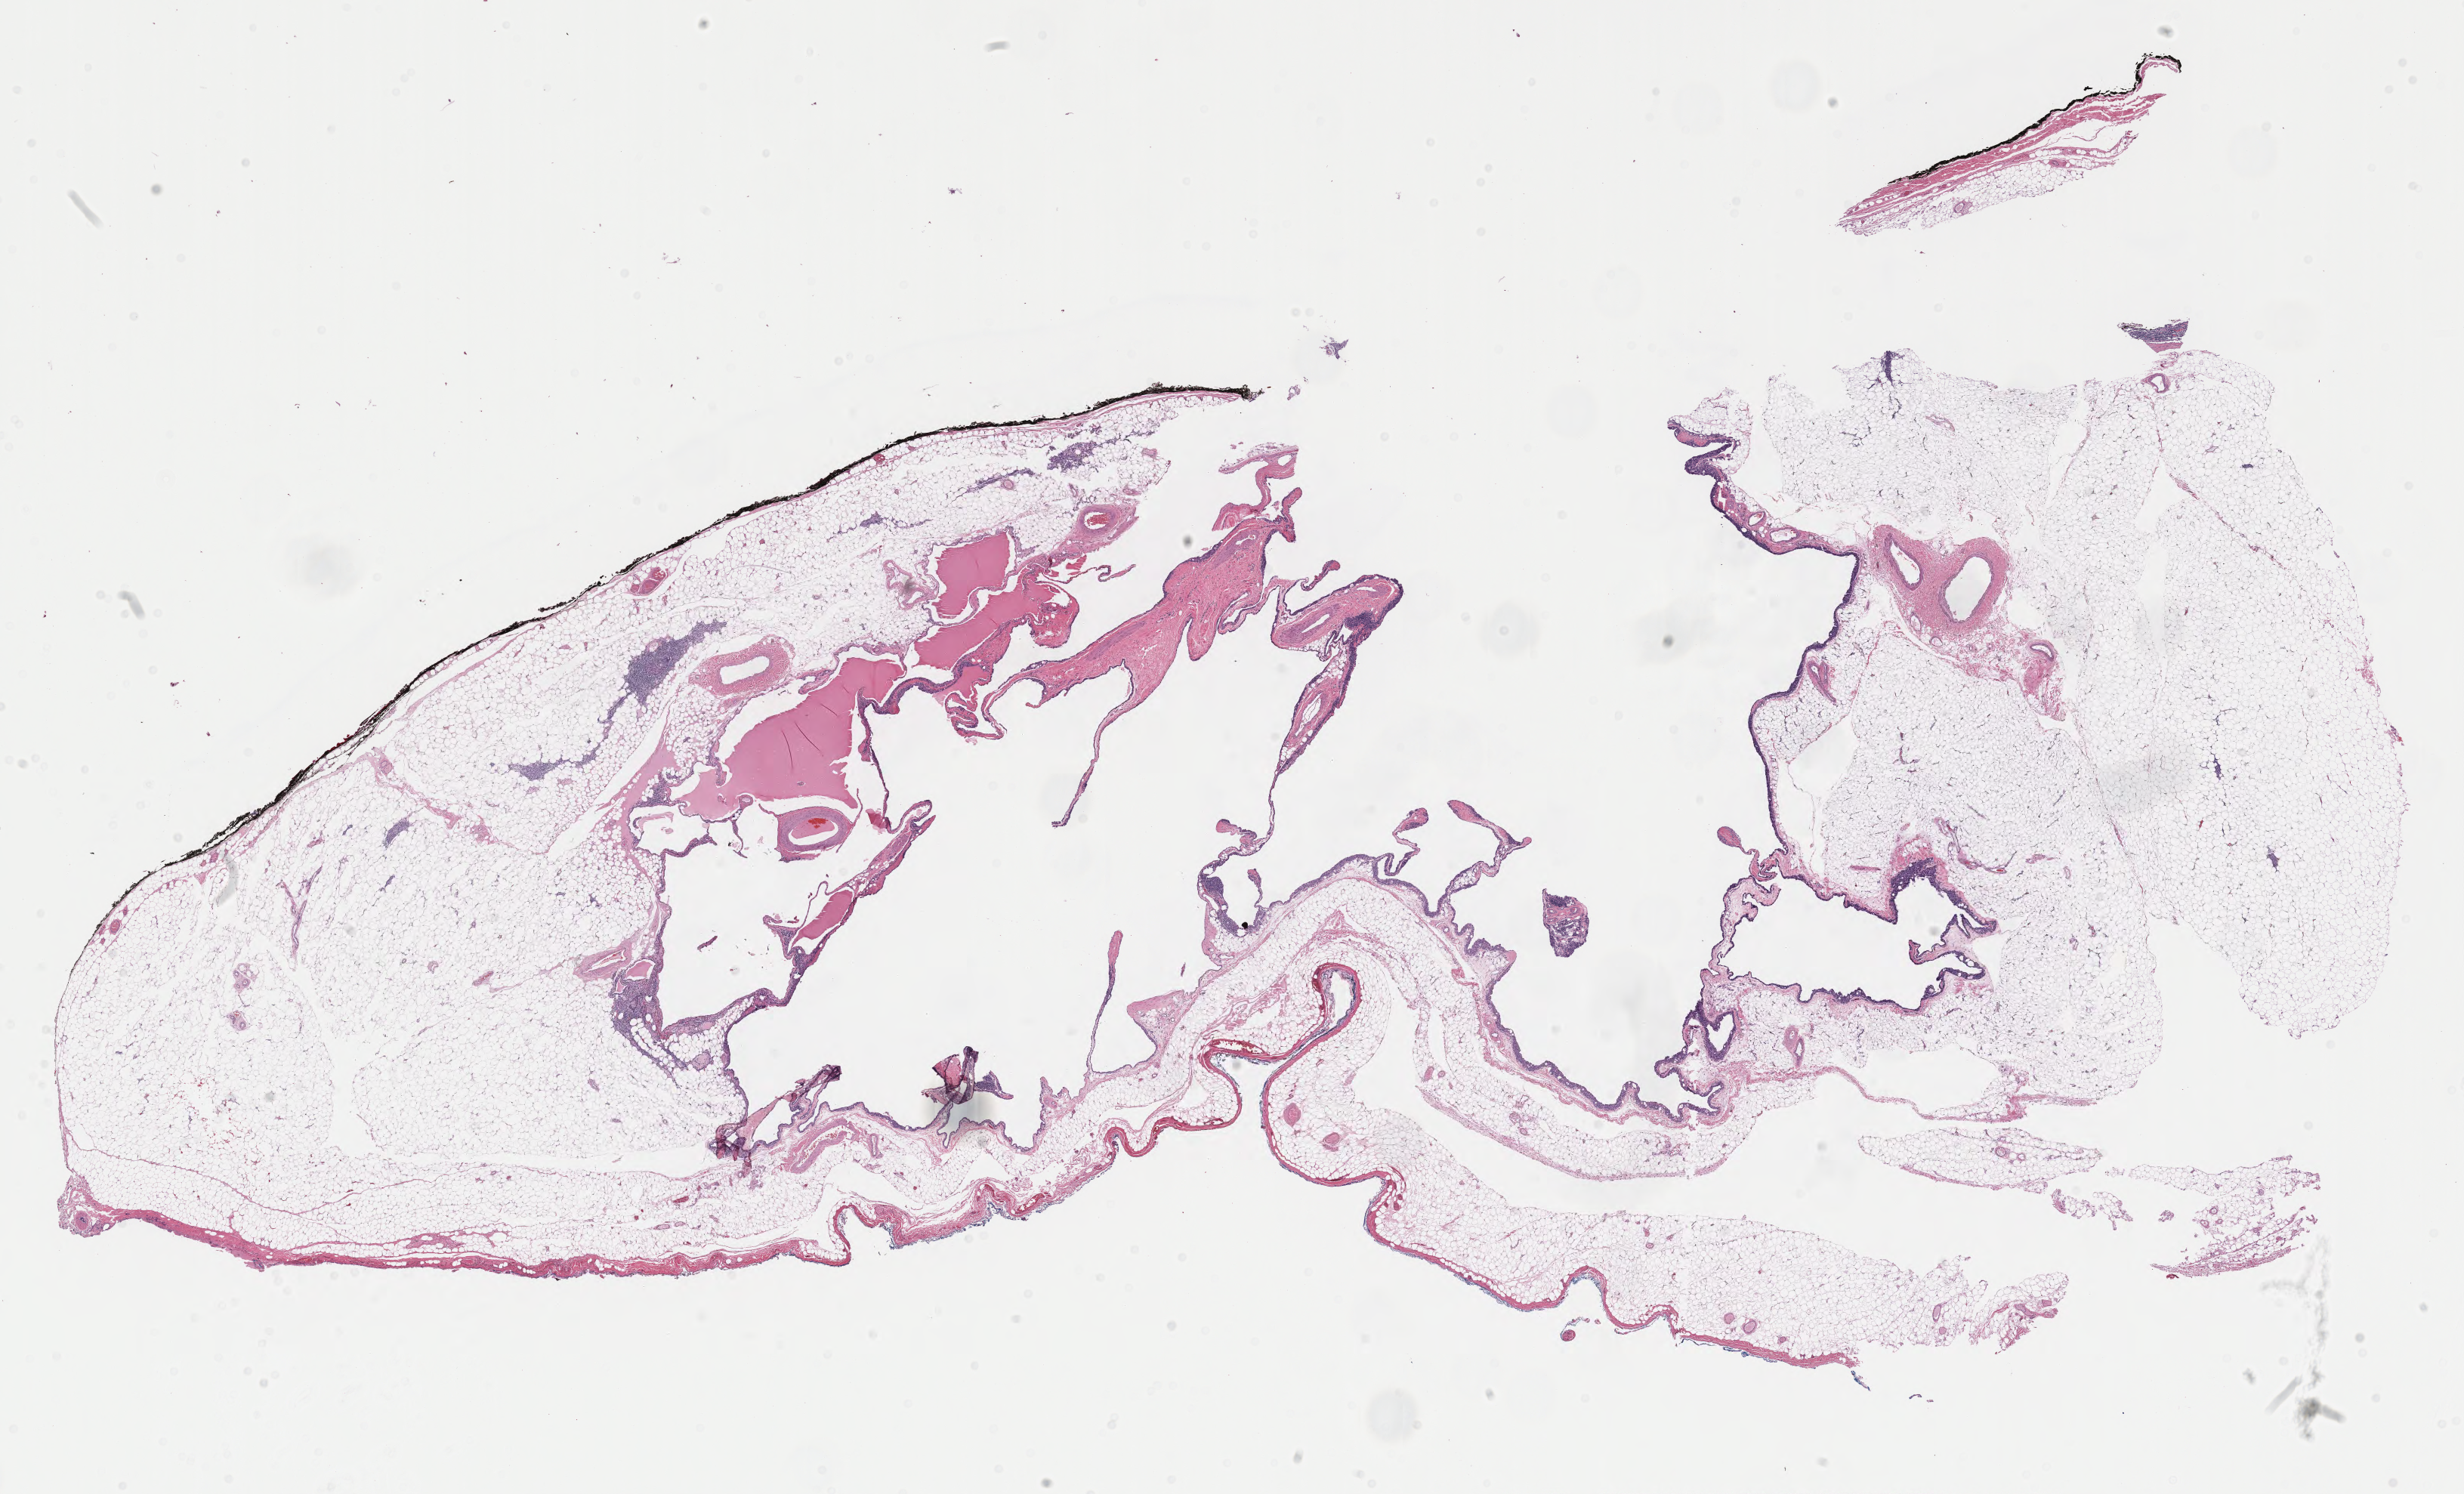
Digitized H&E tissue section (whole slide), shown as a low-resolution overview of the whole scanned area (about 25.9 x 15.7 mm, from a 40x scan), formalin-fixed paraffin-embedded (FFPE) diagnostic section, thymus, primary tumour sample. Male, age 52 years at initial diagnosis.
Diagnosis: Thymoma, type A, malignant.